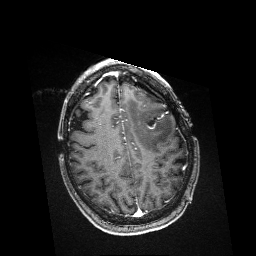
Brain MRI from a brain-tumour surgery series, one axial slice. Slice 121 of 176 in the series (ordered by position). T1-weighted post-contrast. 256 × 256 image matrix, field of view 256 × 256 mm. Case-level facts recorded for this patient, not image findings: histopathology: Metastatic Melanoma; tumour location: Left Frontal.
Outlined on this slice (expert manual segmentation):
- residual tumour: box from (x=148, y=125) to (x=155, y=129) px